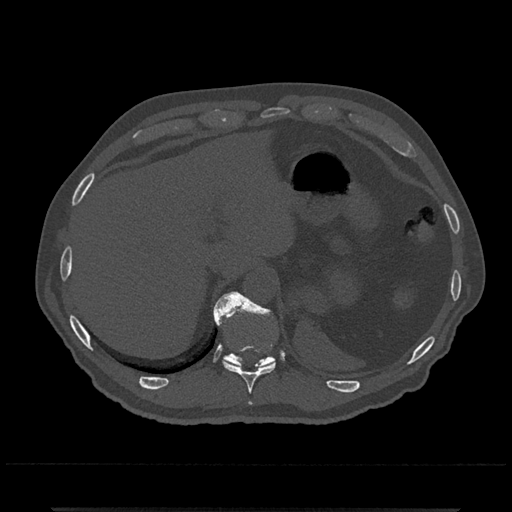
CT including the spine, one axial slice. Slice 531 of 797 in the series (ordered by position). Reconstruction kernel Br40s/3. 120 kVp. Bone window (W 1800 / L 400 HU). 0.5 mm slice thickness. 512 × 512 image matrix, field of view 393 × 393 mm. Male patient, age 67 years. Case-level facts recorded for this patient, not image findings: primary cancer: prostate.
Annotated regions visible in this slice (semi-automatic segmentation, software-assisted and operator-edited):
- T10 vertebra: bounding box [x1, y1, x2, y2] px = [216, 292, 276, 405]
- T11 vertebra: [213, 291, 276, 367]